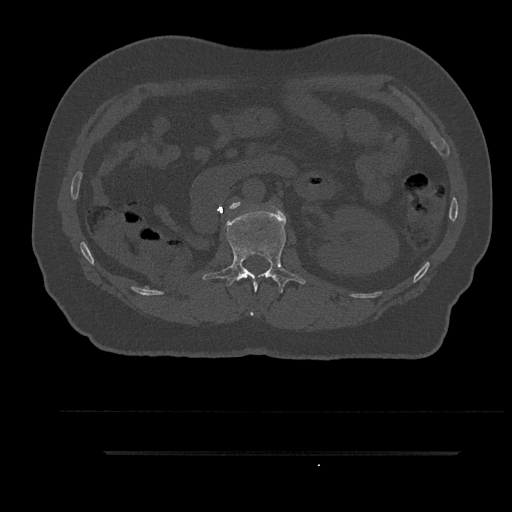
CT including the spine, one axial slice; slice 173 of 797 in the series (ordered by position); reconstruction kernel Br40s/3; bone window (W 1800 / L 400 HU); 0.5 mm slice thickness; 512 × 512 image matrix, field of view 432 × 432 mm. Patient: male, 63 years. From the clinical record (not read from this slice): primary cancer: renal.
Structures marked on this image (semi-automatic segmentation, software-assisted and operator-edited):
- L1 vertebra: bounding box [x1, y1, x2, y2] px = [203, 206, 305, 315]
- L2 vertebra: [230, 202, 240, 209]